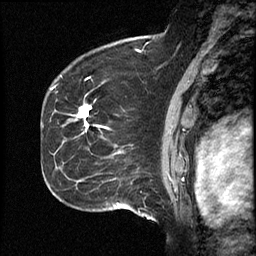
Breast MRI (dynamic contrast-enhanced), one sagittal slice. Slice 32 of 46 in the series (ordered by position). Dynamic contrast-enhanced study with each time point stored as its own series, time point 2 of 4 at this slice position (early post-contrast, ordered by acquisition time). 1.5 T. TE 4.2 ms, TR 18.3 ms. 3 mm slice thickness. 256 × 256 image matrix, field of view 200 × 200 mm. Case-level facts recorded for this patient, not image findings: setting: breast cancer imaged before/during neoadjuvant chemotherapy; receptor status: HR-positive, HER2-negative.
Structures marked on this image (semi-automatic segmentation, software-assisted and operator-edited):
- analysis volume of interest (the breast-tissue region the enhancement analysis was run in; not a lesion): bounding box (x1, y1, x2, y2) in pixels: (64, 71, 111, 209)
- tumour enhancement mask (voxels above the 100 % enhancement threshold inside the analysis volume of interest): (79, 105, 91, 127)